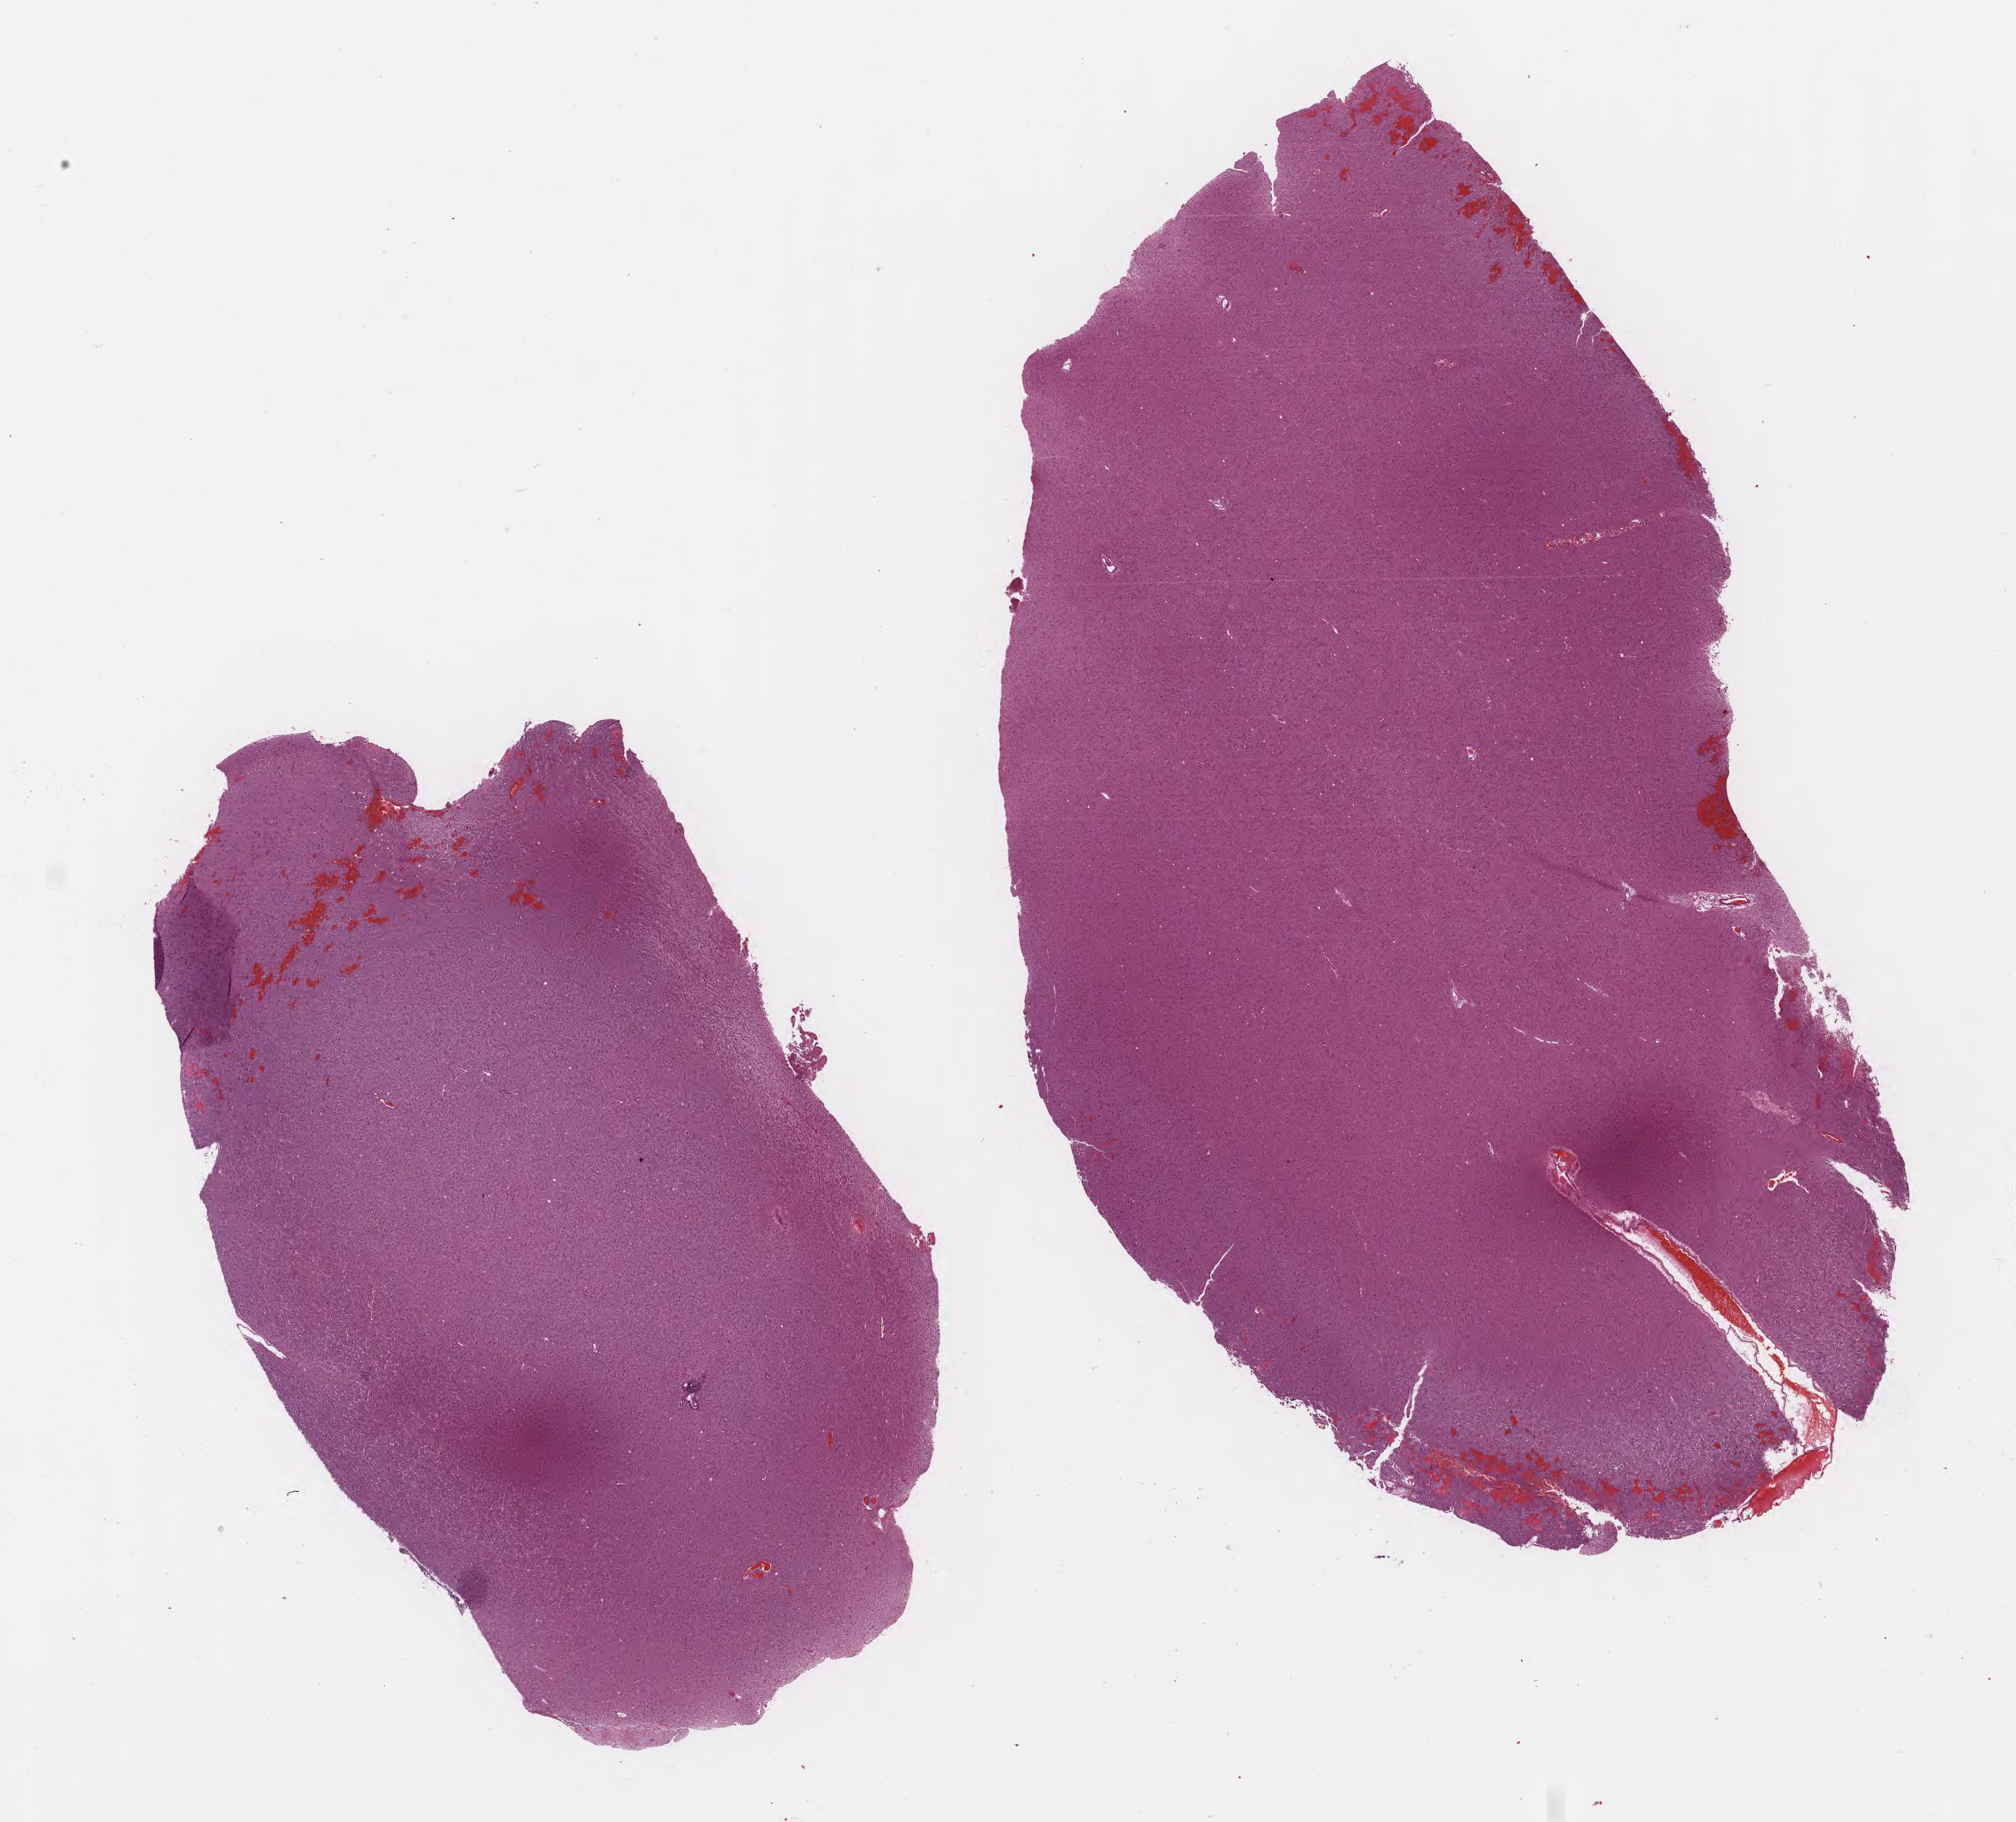
H&E whole-slide image — shown as a low-resolution overview of the whole scanned area (about 20.6 x 18.7 mm, acquisition: 40x scan). Formalin-fixed paraffin-embedded (FFPE) diagnostic section. Primary tumour sample from the brain. Patient: male, age at initial diagnosis 38 years.
Diagnosis: Oligodendroglioma, NOS (cerebrum).